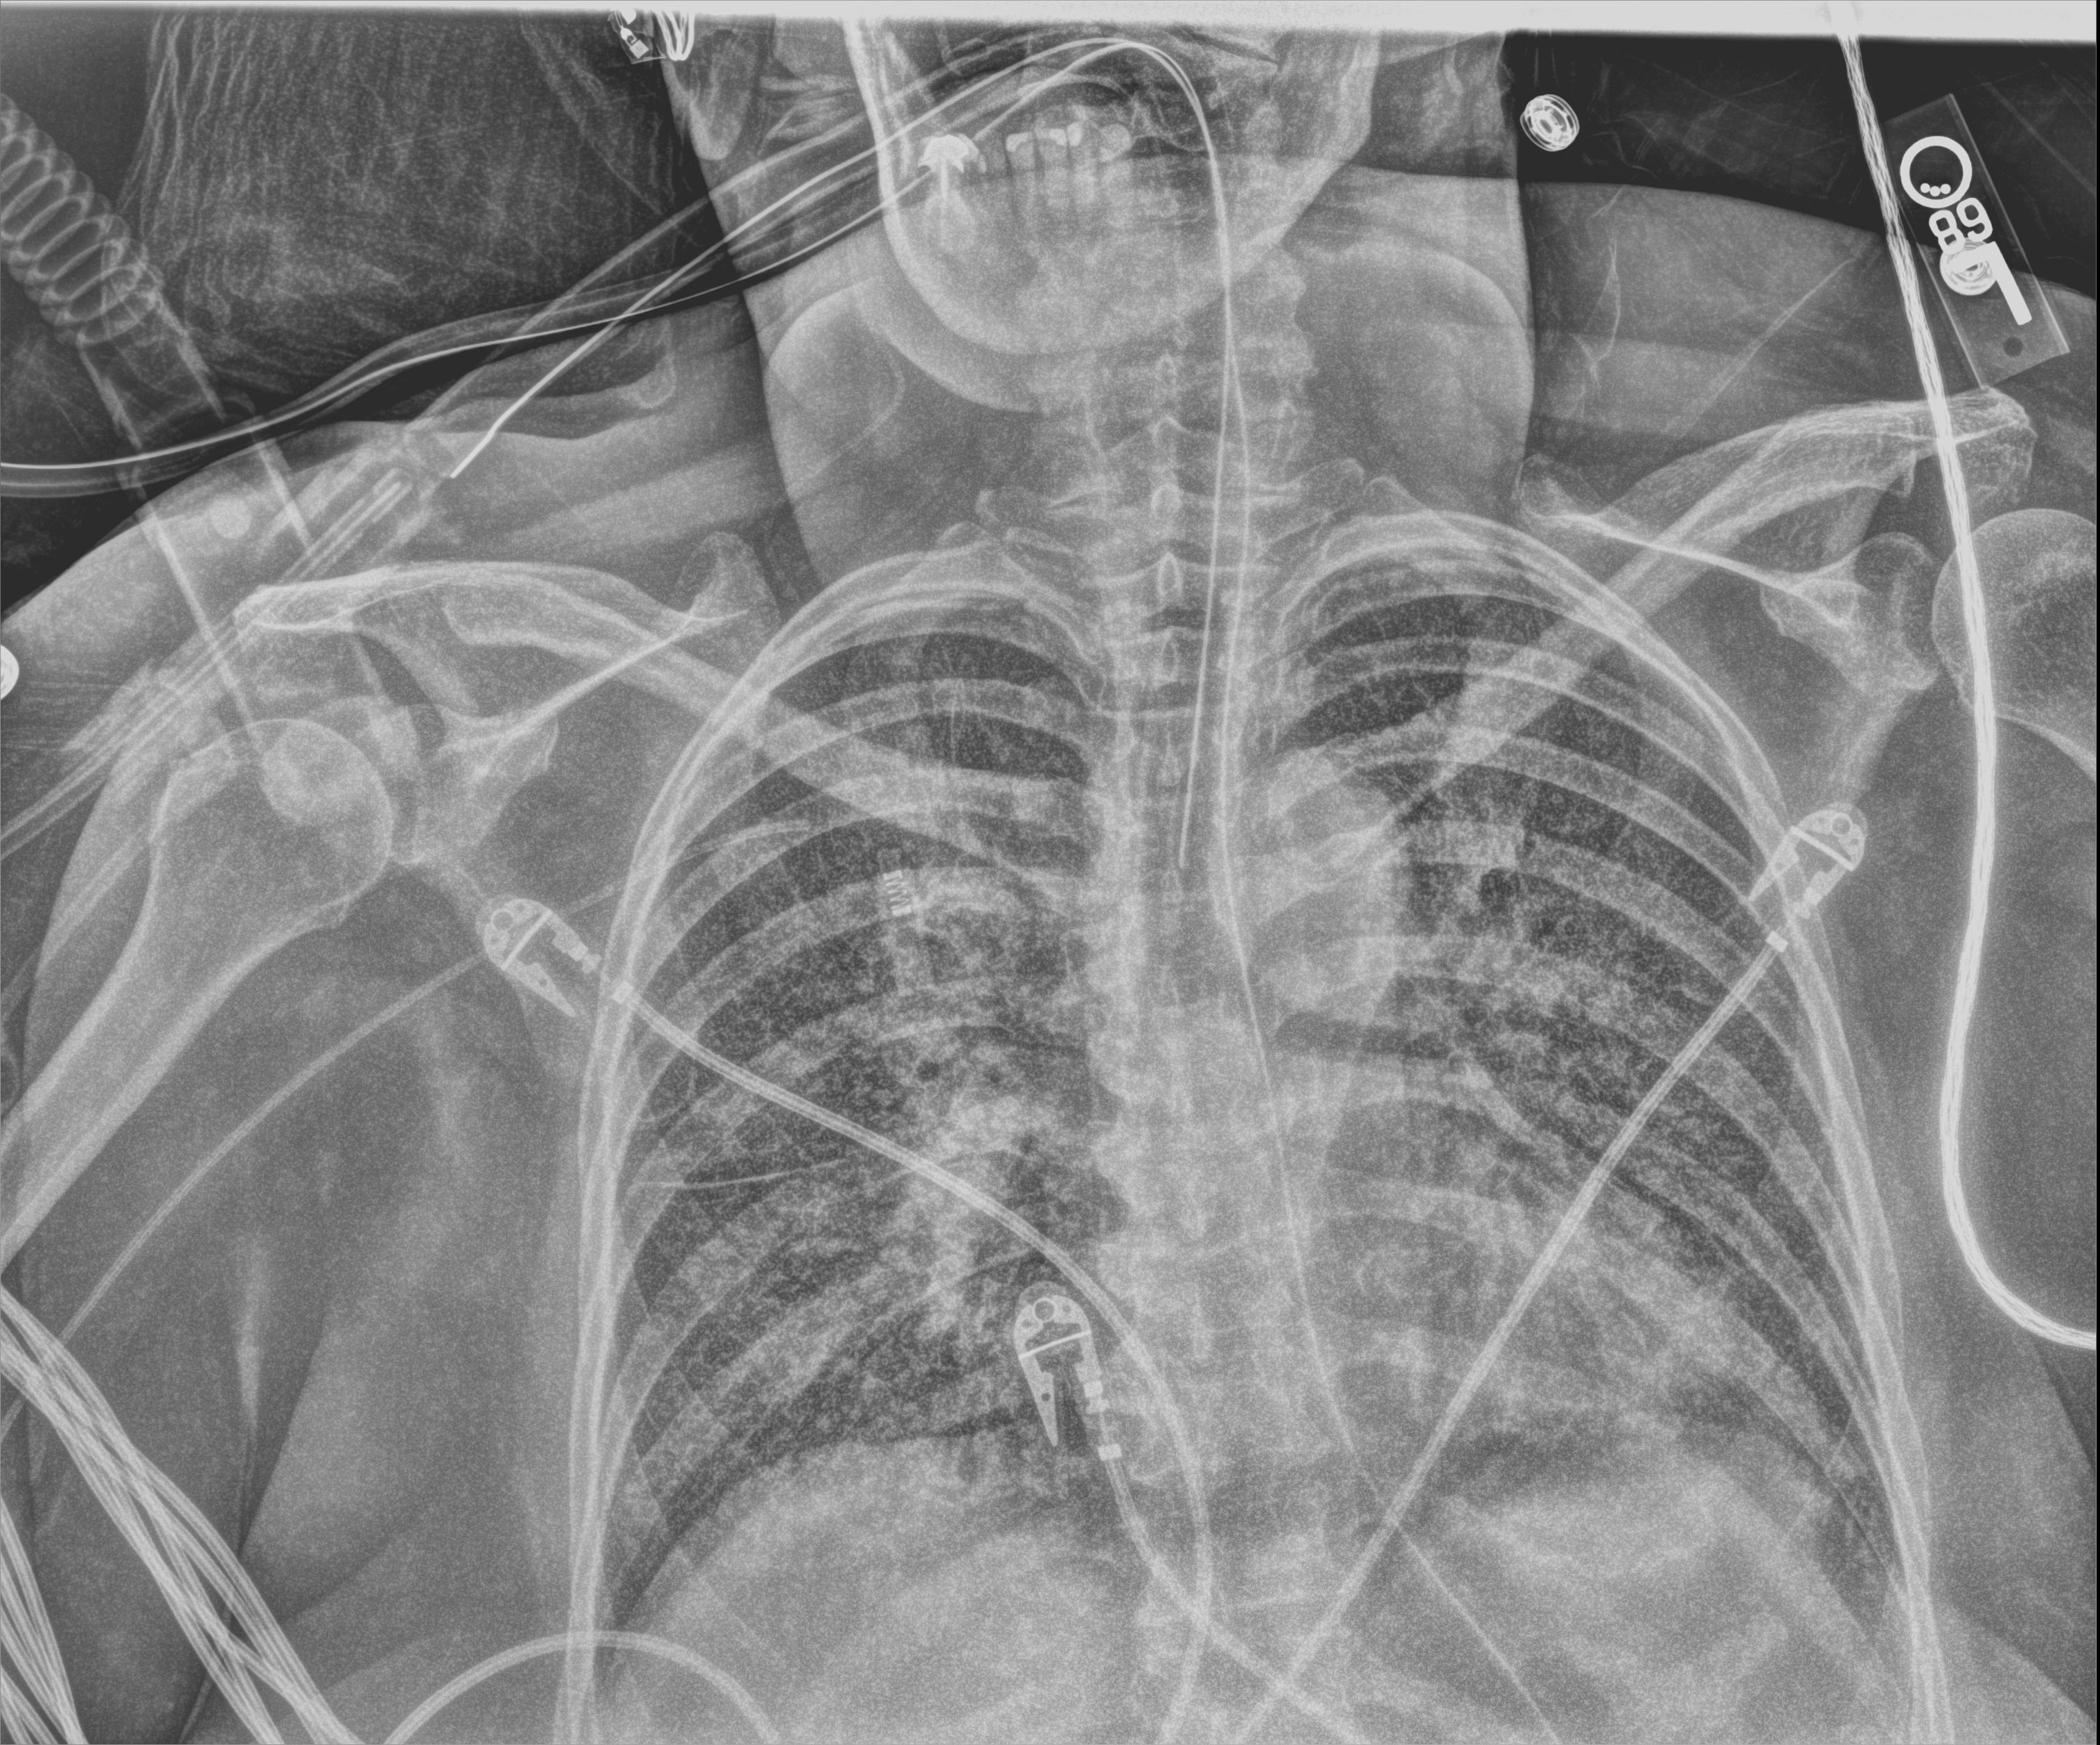
Chest X-ray; anteroposterior (AP) projection. Female patient hospitalised with COVID-19, age 60–74 years.
Hospital-stay facts (about this admission, not read from this image; timing relative to this image not recorded): chronic kidney disease (admission record): no.